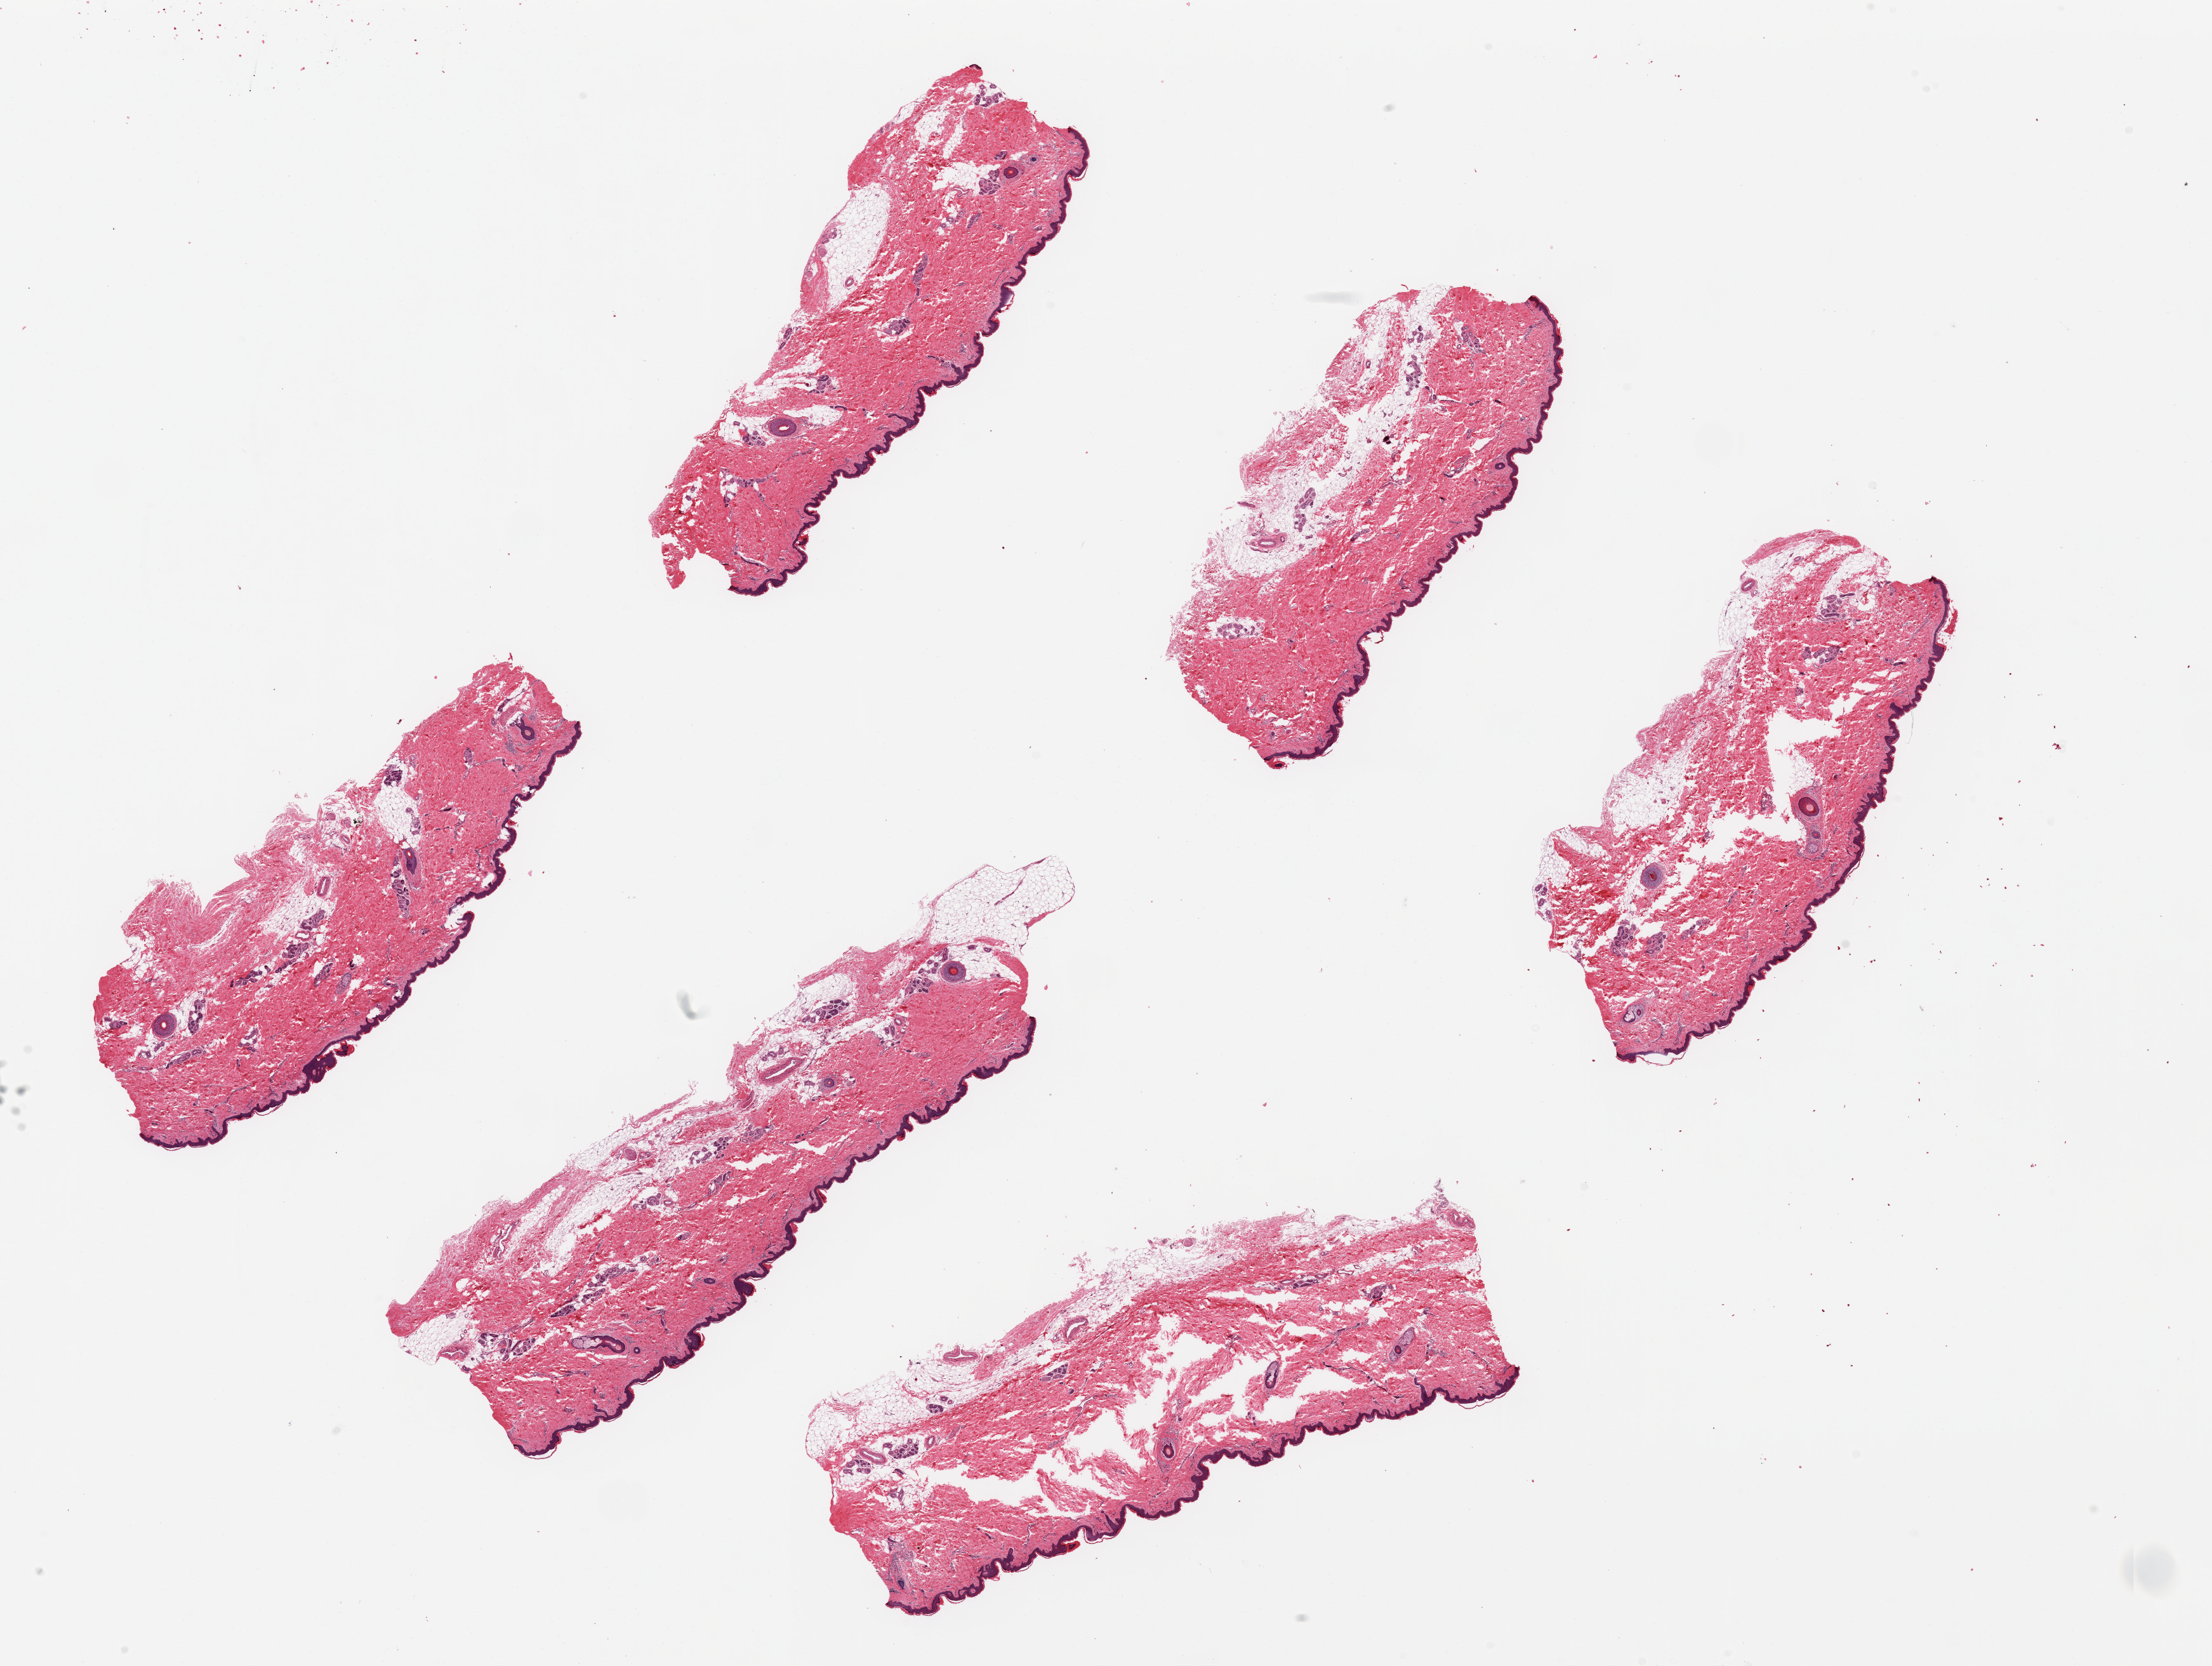
Digitized hematoxylin and eosin (H&E)-stained section, whole scanned area (about 27.6 x 20.8 mm, acquisition: 20x scan) shown as a low-resolution overview, PAXgene-fixed paraffin-embedded (PFPE) section, target tissue: skin of lower leg, donor tissue sample. Male donor.
Reviewer comment on this tissue sample: 6 pieces~8.5x2.5mm; many sweat and sebaceous glands; tissue tears.